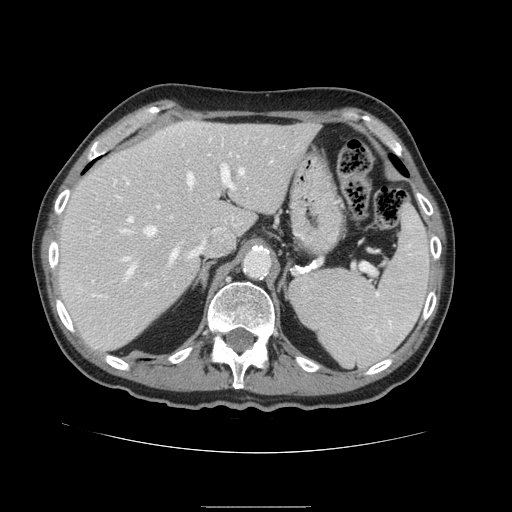
Contrast-enhanced abdominal CT, one axial slice. Slice 107 of 168 in the series (ordered by position). Soft-tissue window (W 400 / L 40 HU). 512 × 512 image matrix, field of view 386 × 386 mm. Male patient, age 74 years. From the clinical record (not read from this slice): diagnosis: colorectal cancer liver metastases, imaged before liver resection; multiple liver metastases: no; largest metastasis: 14.5 cm; chemotherapy before resection: no.
Annotated regions visible in this slice (expert manual segmentation):
- hepatic veins: box from (x=125, y=168) to (x=244, y=276) px
- liver: (x=58, y=121)–(x=320, y=351)
- planned liver remnant (the part of the liver to remain after resection): (x=58, y=121)–(x=320, y=351)
- portal vein (with intrahepatic branches): (x=94, y=167)–(x=233, y=259)